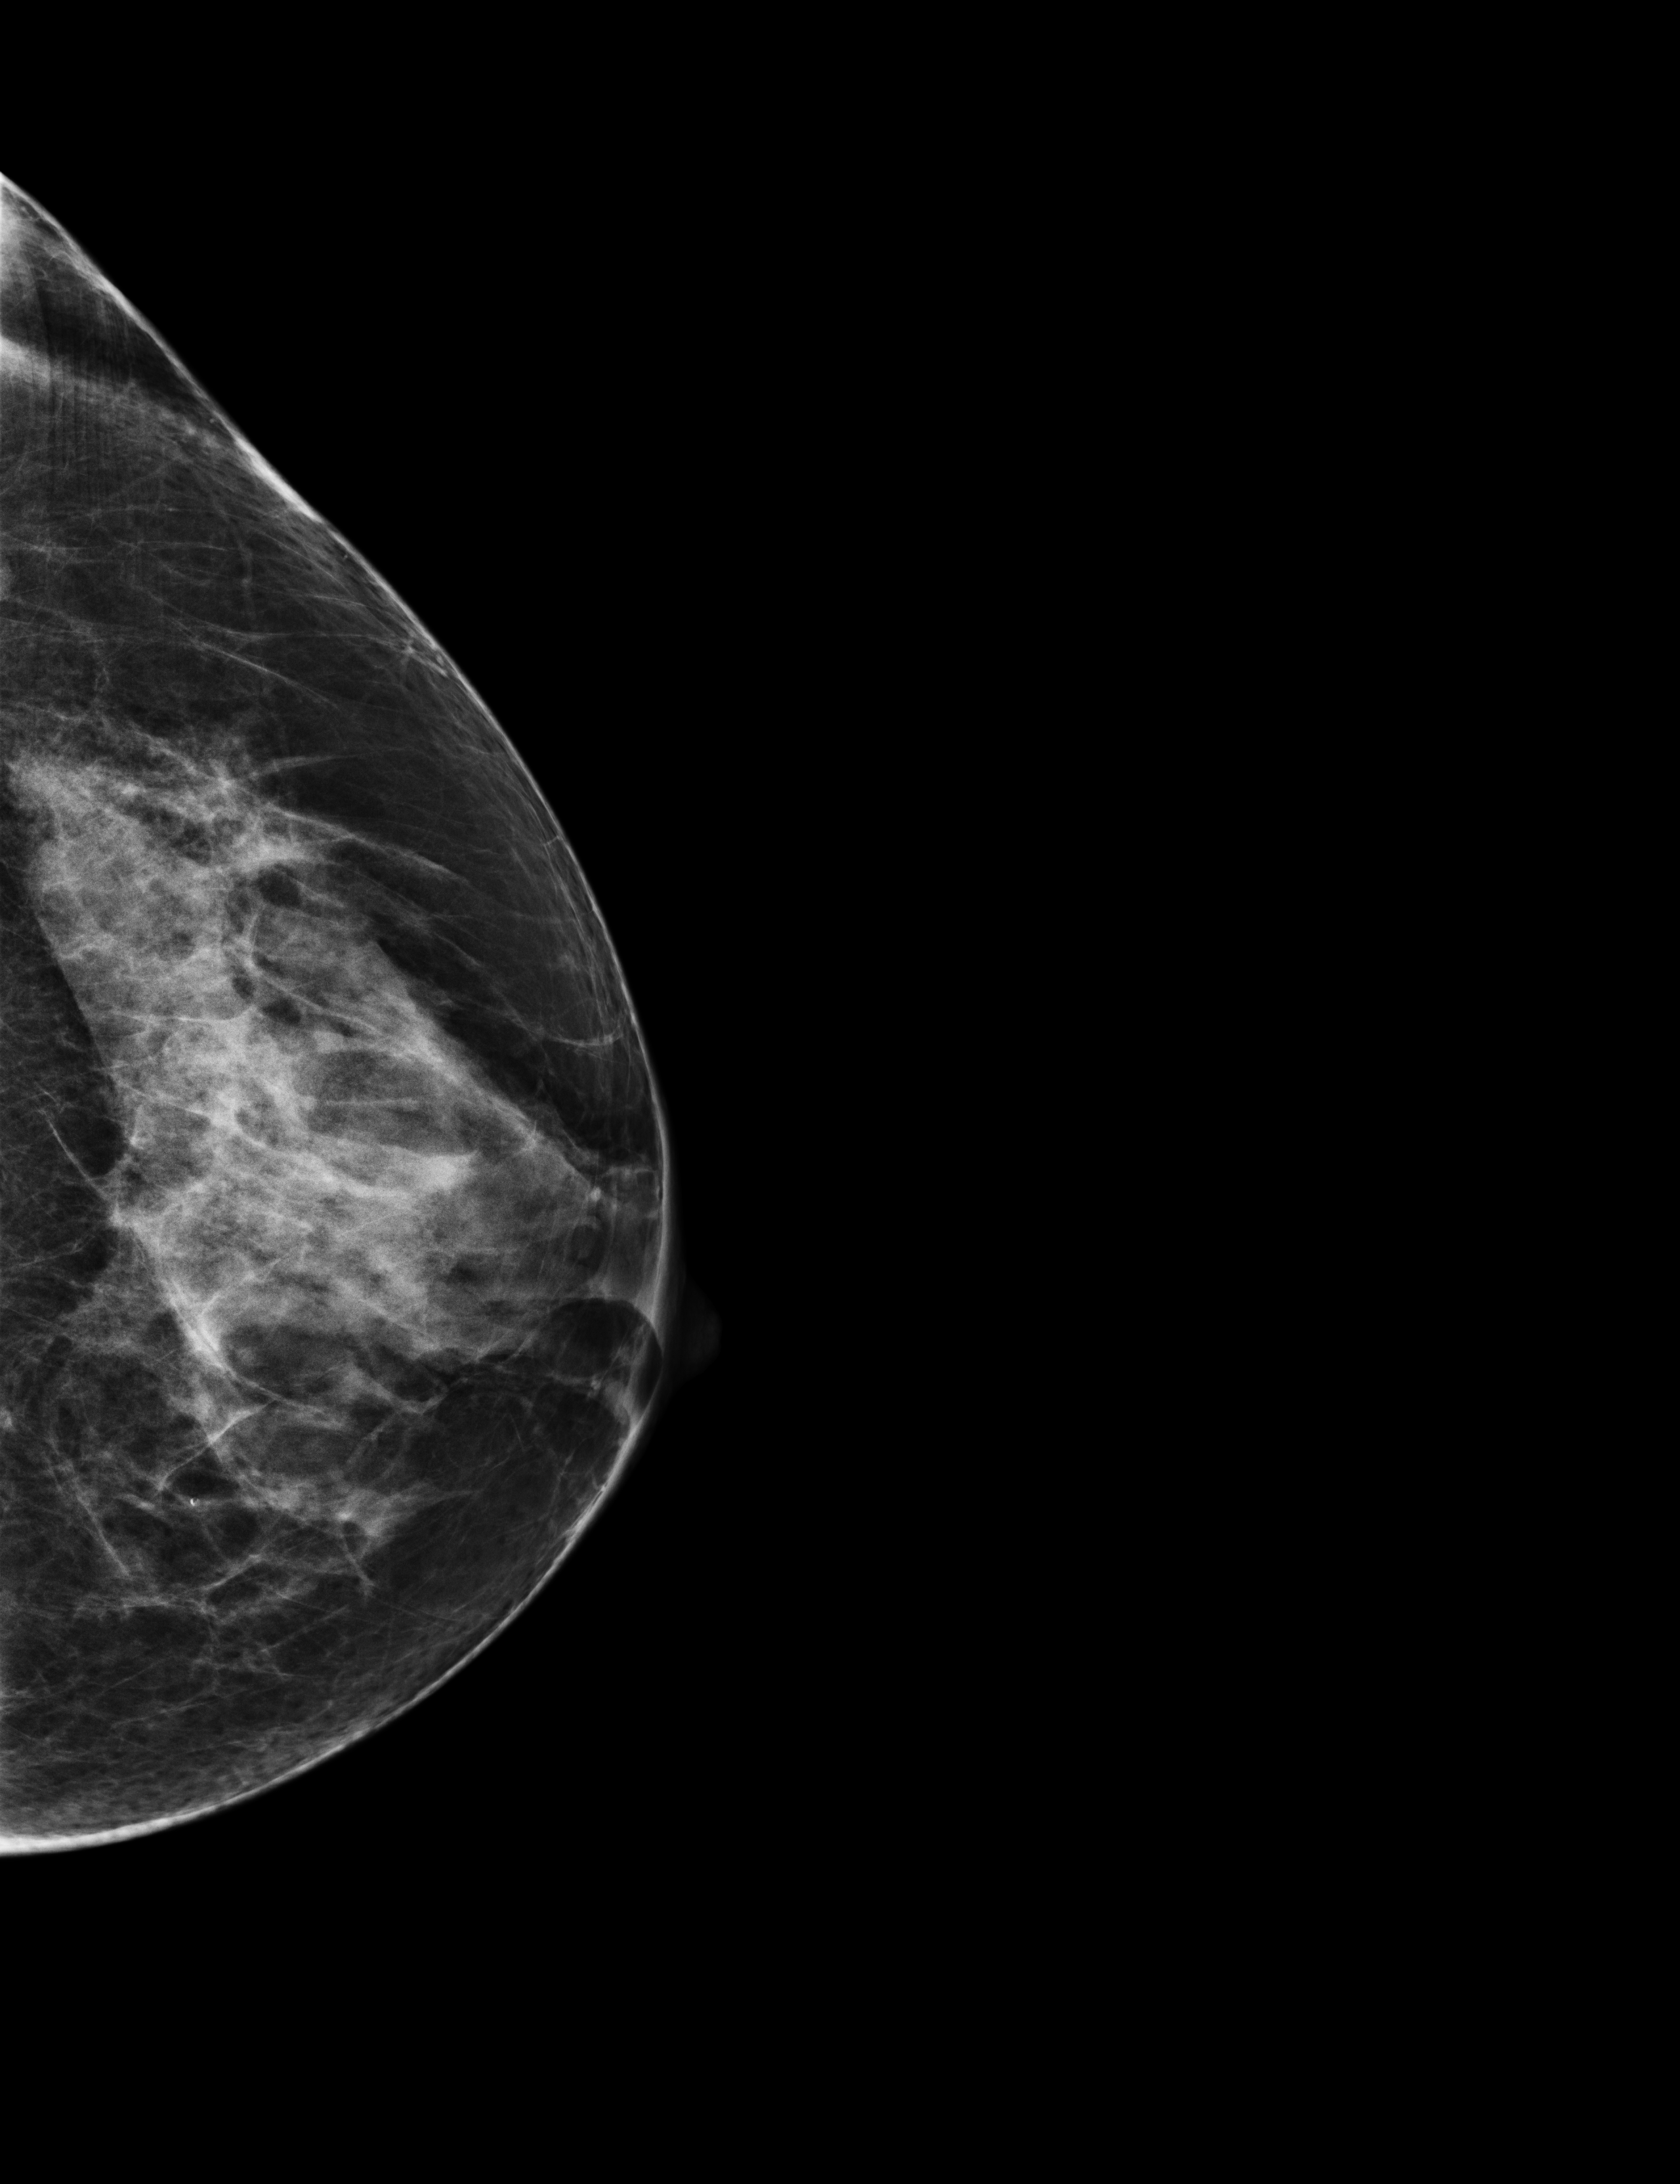
Screening examination; compressed breast thickness 64 mm. Patient: female, 59 years.
Image type: full-field digital mammogram. Breast: left. Projection: craniocaudal (CC) view. Breast density at the screening exam (both breasts): heterogeneously dense (BI-RADS density category c). Final BI-RADS category for the screening round (tomosynthesis exam, both breasts): category 2. Recall: no recall after this screen.